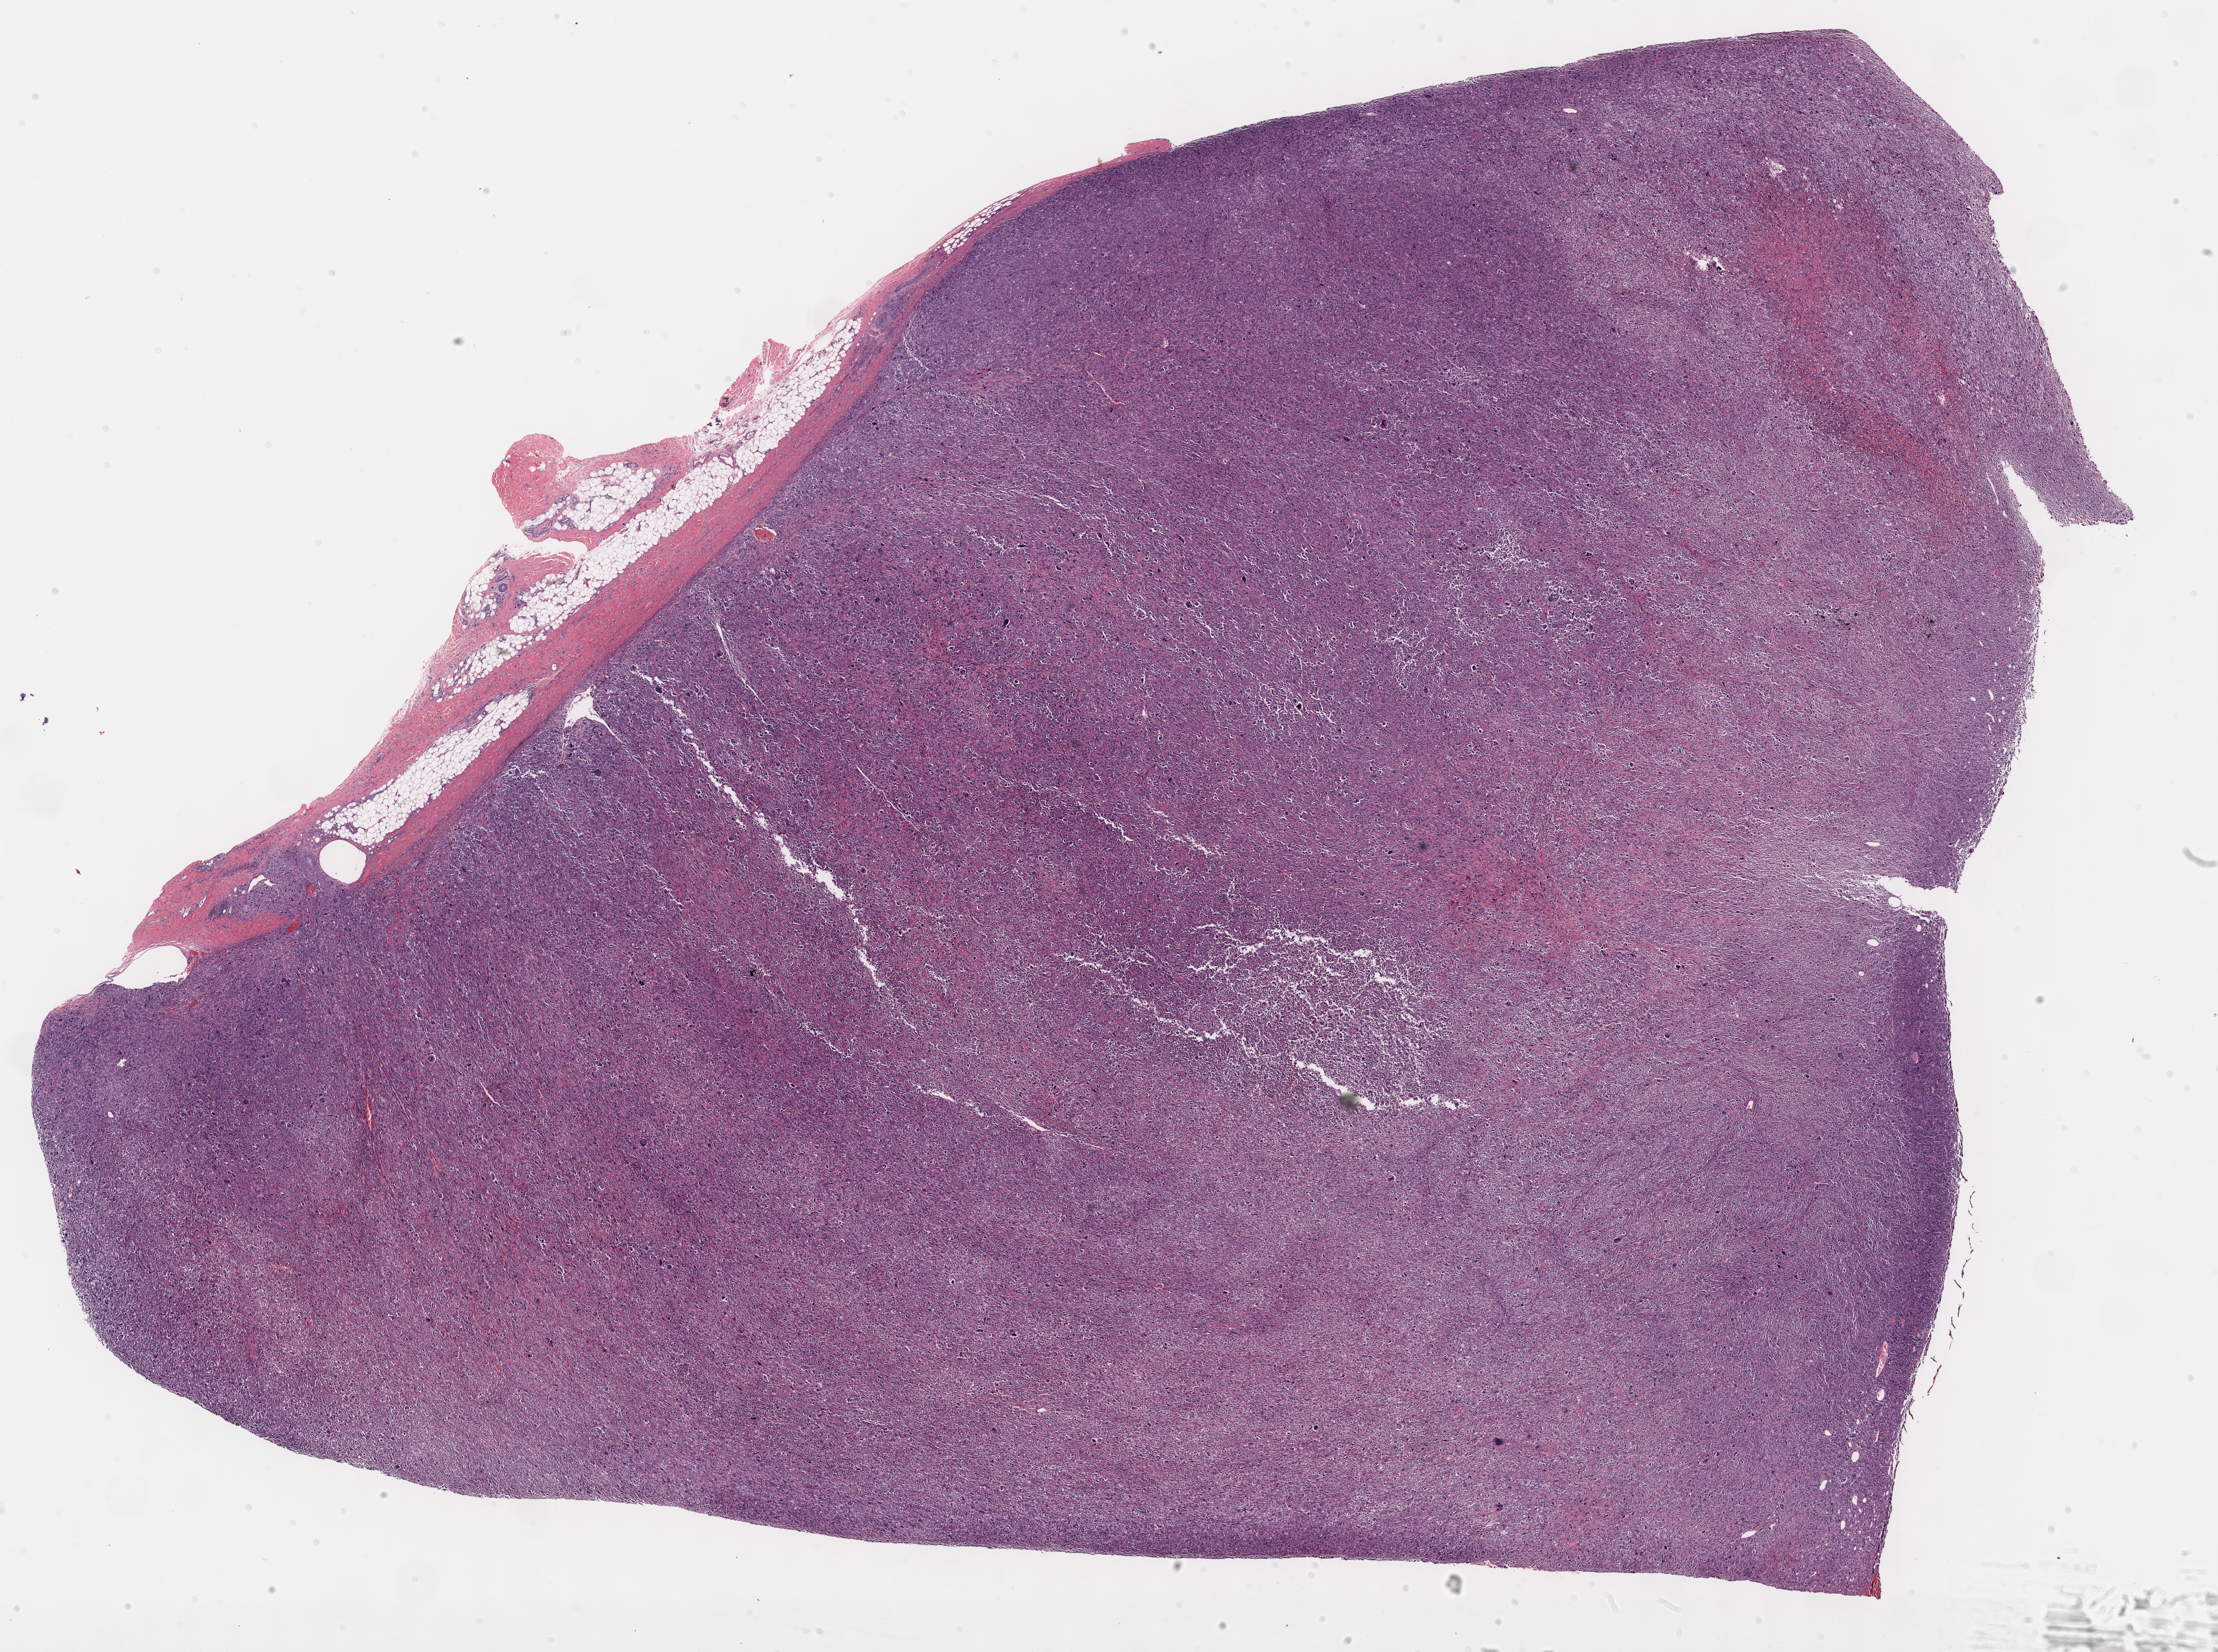
H&E whole-slide image, shown as a low-resolution overview of the whole scanned area (about 26.2 x 19.5 mm, slide scanned at 40x), formalin-fixed paraffin-embedded (FFPE) diagnostic section, primary tumour sample from the connective, subcutaneous and other soft tissues. Patient: female, age at initial diagnosis 78 years.
Histologic diagnosis: Malignant fibrous histiocytoma (connective, subcutaneous and other soft tissues of lower limb and hip).